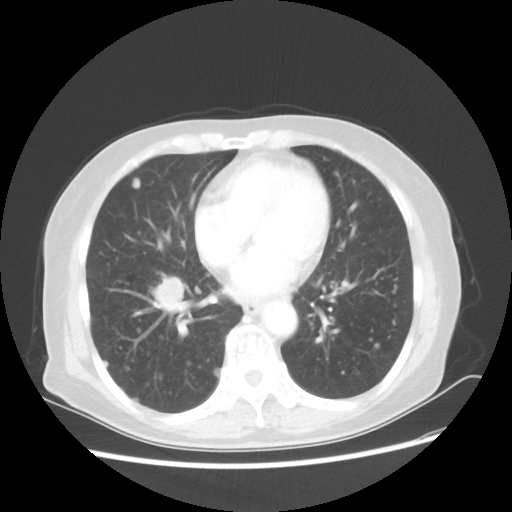
Chest CT, one axial slice; 80 kVp; lung window (W 1500 / L -600 HU); 512 × 512 image matrix, field of view 360 × 360 mm. Female patient, age 68 years. Case-level facts recorded for this patient, not image findings: clinical TNM (as recorded): T1c N3 M0.
Outlined on this slice (bounding box drawn by a radiologist):
- lung tumour (recorded histology: squamous cell carcinoma): bounding box [x1, y1, x2, y2] px = [144, 268, 185, 312]